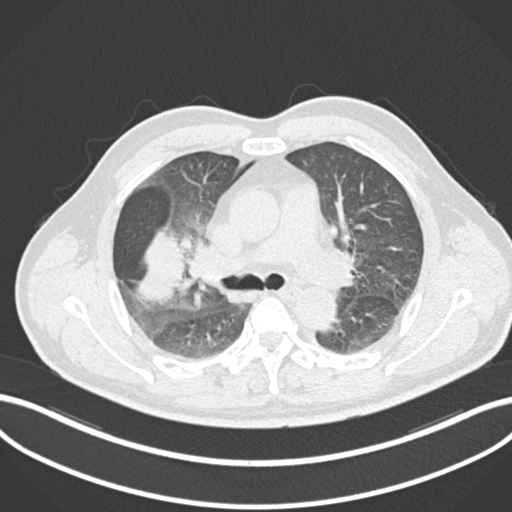
Chest CT, one axial slice. Position 645 of 852 along the scan axis. Reconstruction kernel B30f. Lung window (W 1500 / L -600 HU). 1 mm slice thickness. 512 × 512 image matrix, field of view 400 × 400 mm. Patient: male, 55 years. Case-level facts recorded for this patient, not image findings: clinical TNM (as recorded): T3 N2 M1.
Annotated regions visible in this slice (rectangle marked by the reading radiologist):
- lung tumour (recorded histology: adenocarcinoma): box from (x=134, y=229) to (x=191, y=308) px